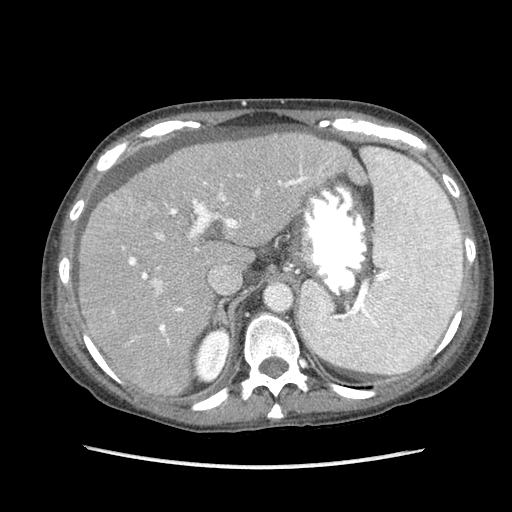
Contrast-enhanced abdominal CT (liver protocol), one axial slice. Slice 62 of 87 in the series (ordered by position). Reconstruction kernel STANDARD. Soft-tissue window (W 400 / L 40 HU). 2.5 mm slice thickness. 512 × 512 image matrix, field of view 340 × 340 mm. Case-level facts recorded for this patient, not image findings: diagnosis: hepatocellular carcinoma (patient treated with transarterial chemoembolisation; whether this scan precedes or follows treatment is not stated here); TNM stage (as recorded): Stage-IIIB; Child-Pugh class: A; tumour differentiation: no biopsy.
Outlined on this slice (semi-automatic segmentation, software-assisted and operator-edited):
- abdominal aorta: box from (x=266, y=285) to (x=291, y=310) px
- liver parenchyma outside the tumour (the mass and vessels are separate outlines, so this box may not span the whole liver): (x=78, y=132)–(x=364, y=394)
- mass: (x=109, y=191)–(x=135, y=216)
- liver vessels: (x=112, y=160)–(x=330, y=343)